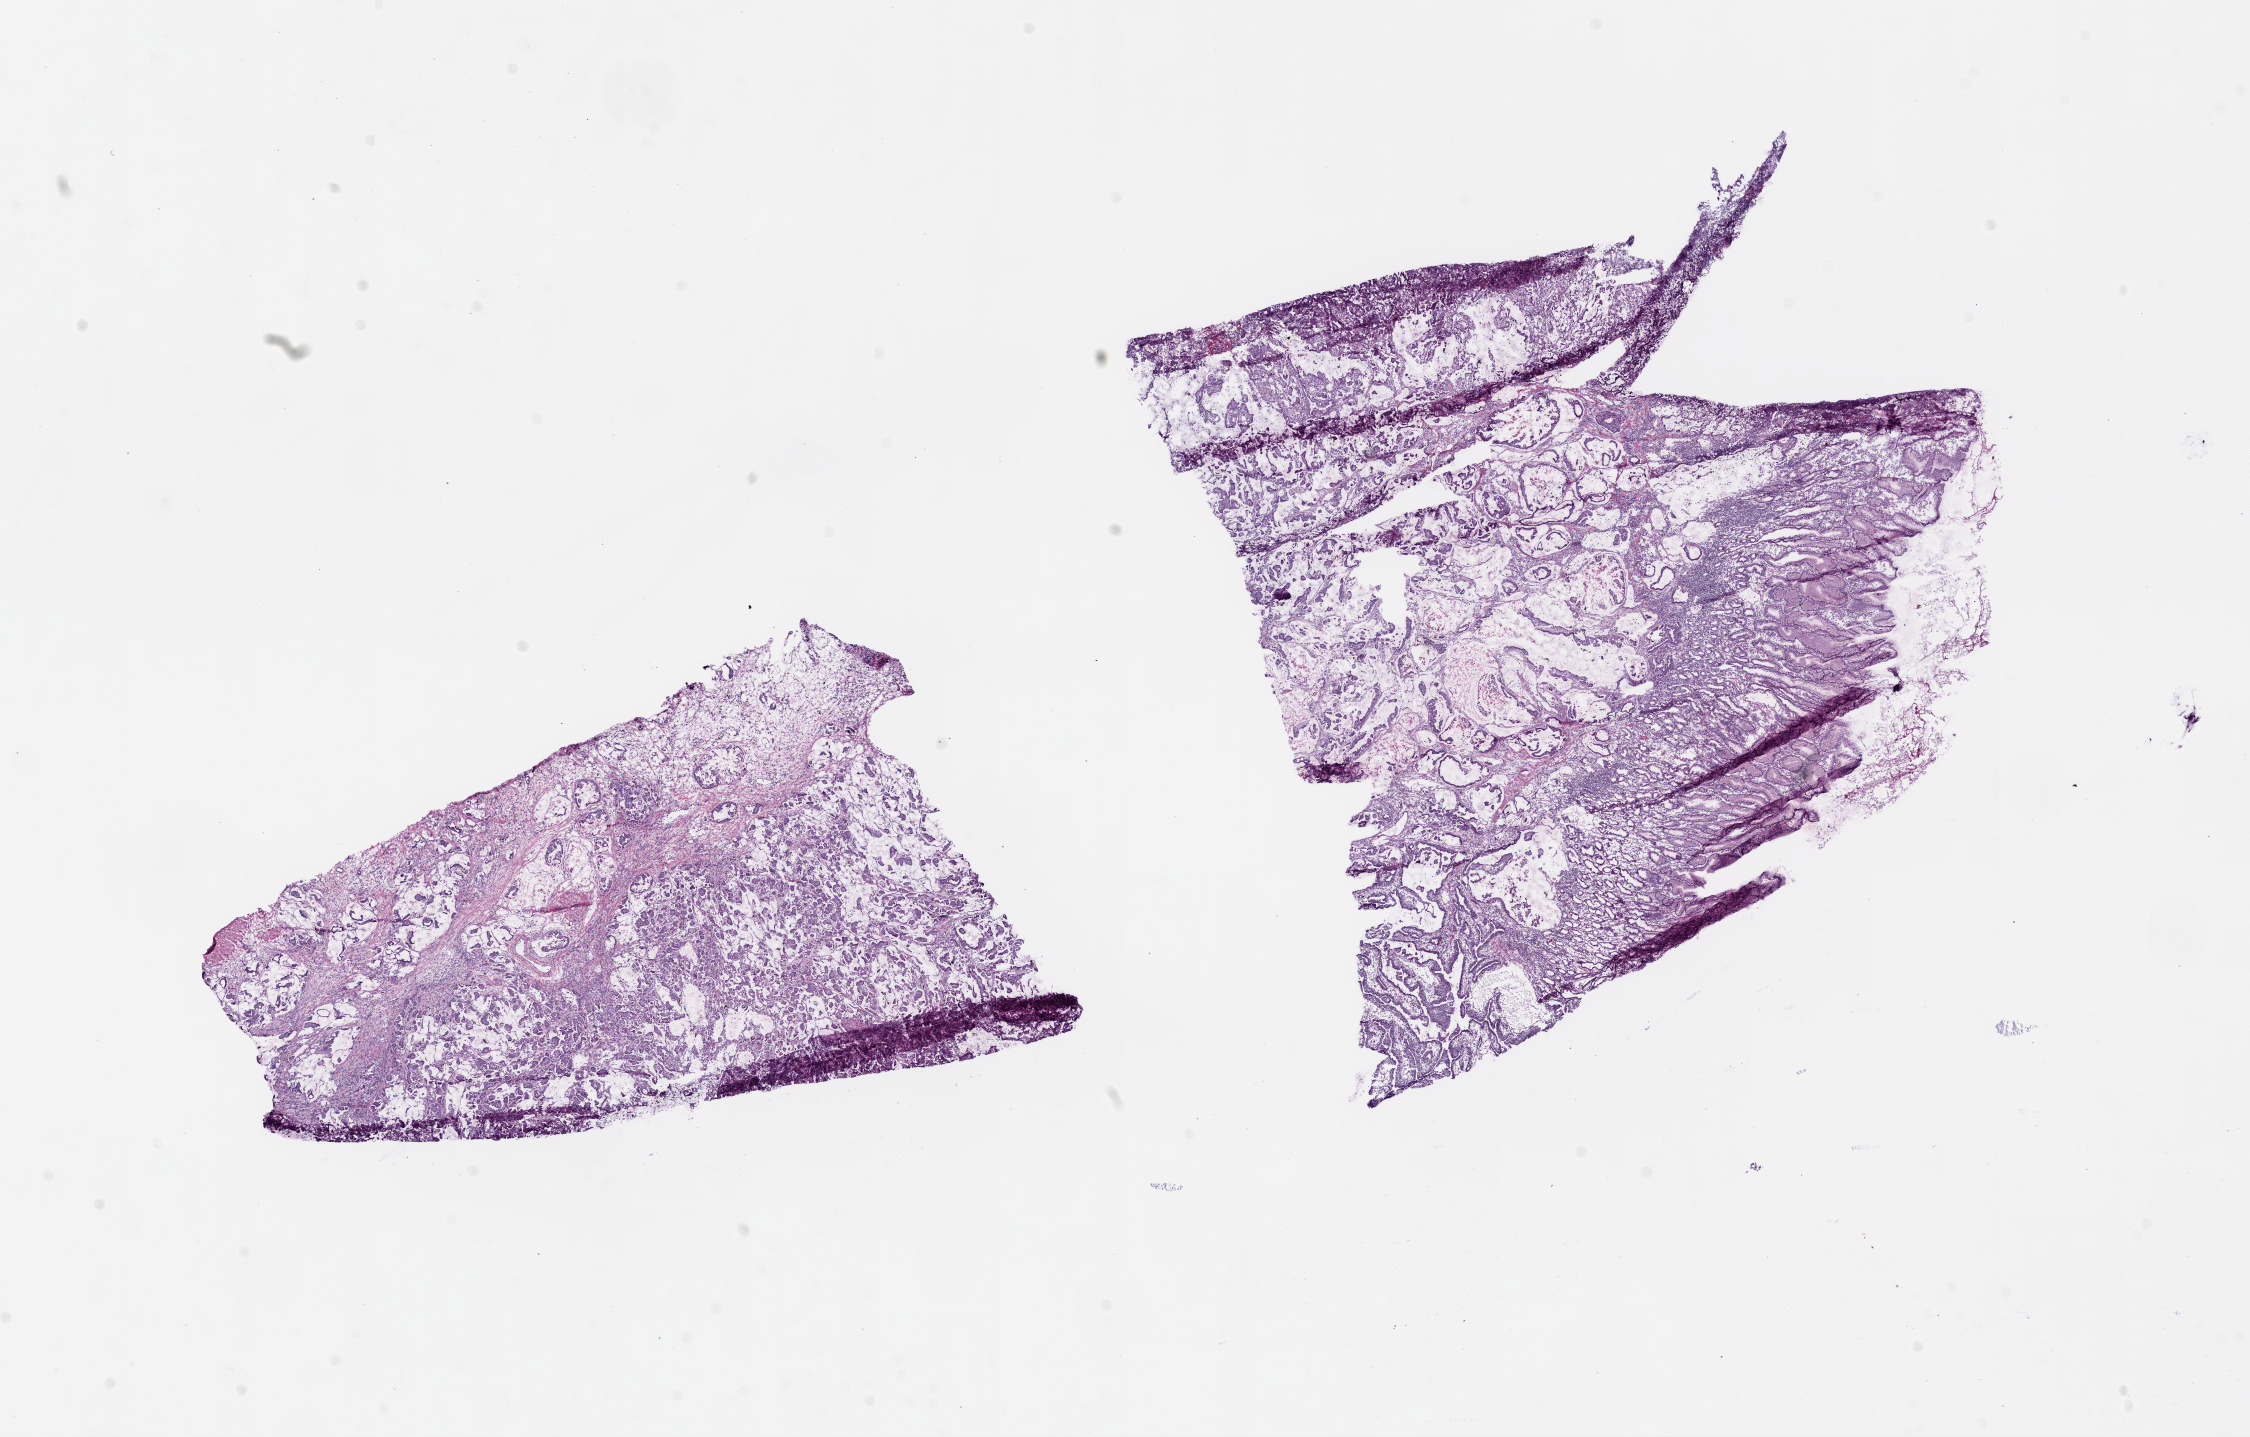
Whole-slide histology image, H&E-stained, whole scanned area (about 18.1 x 11.5 mm) shown as a low-resolution overview. Frozen section from the bottom of the tissue portion. Sample: primary tumour, stomach. Patient sex: male.
Pathologic diagnosis: Adenocarcinoma, NOS (gastric antrum).